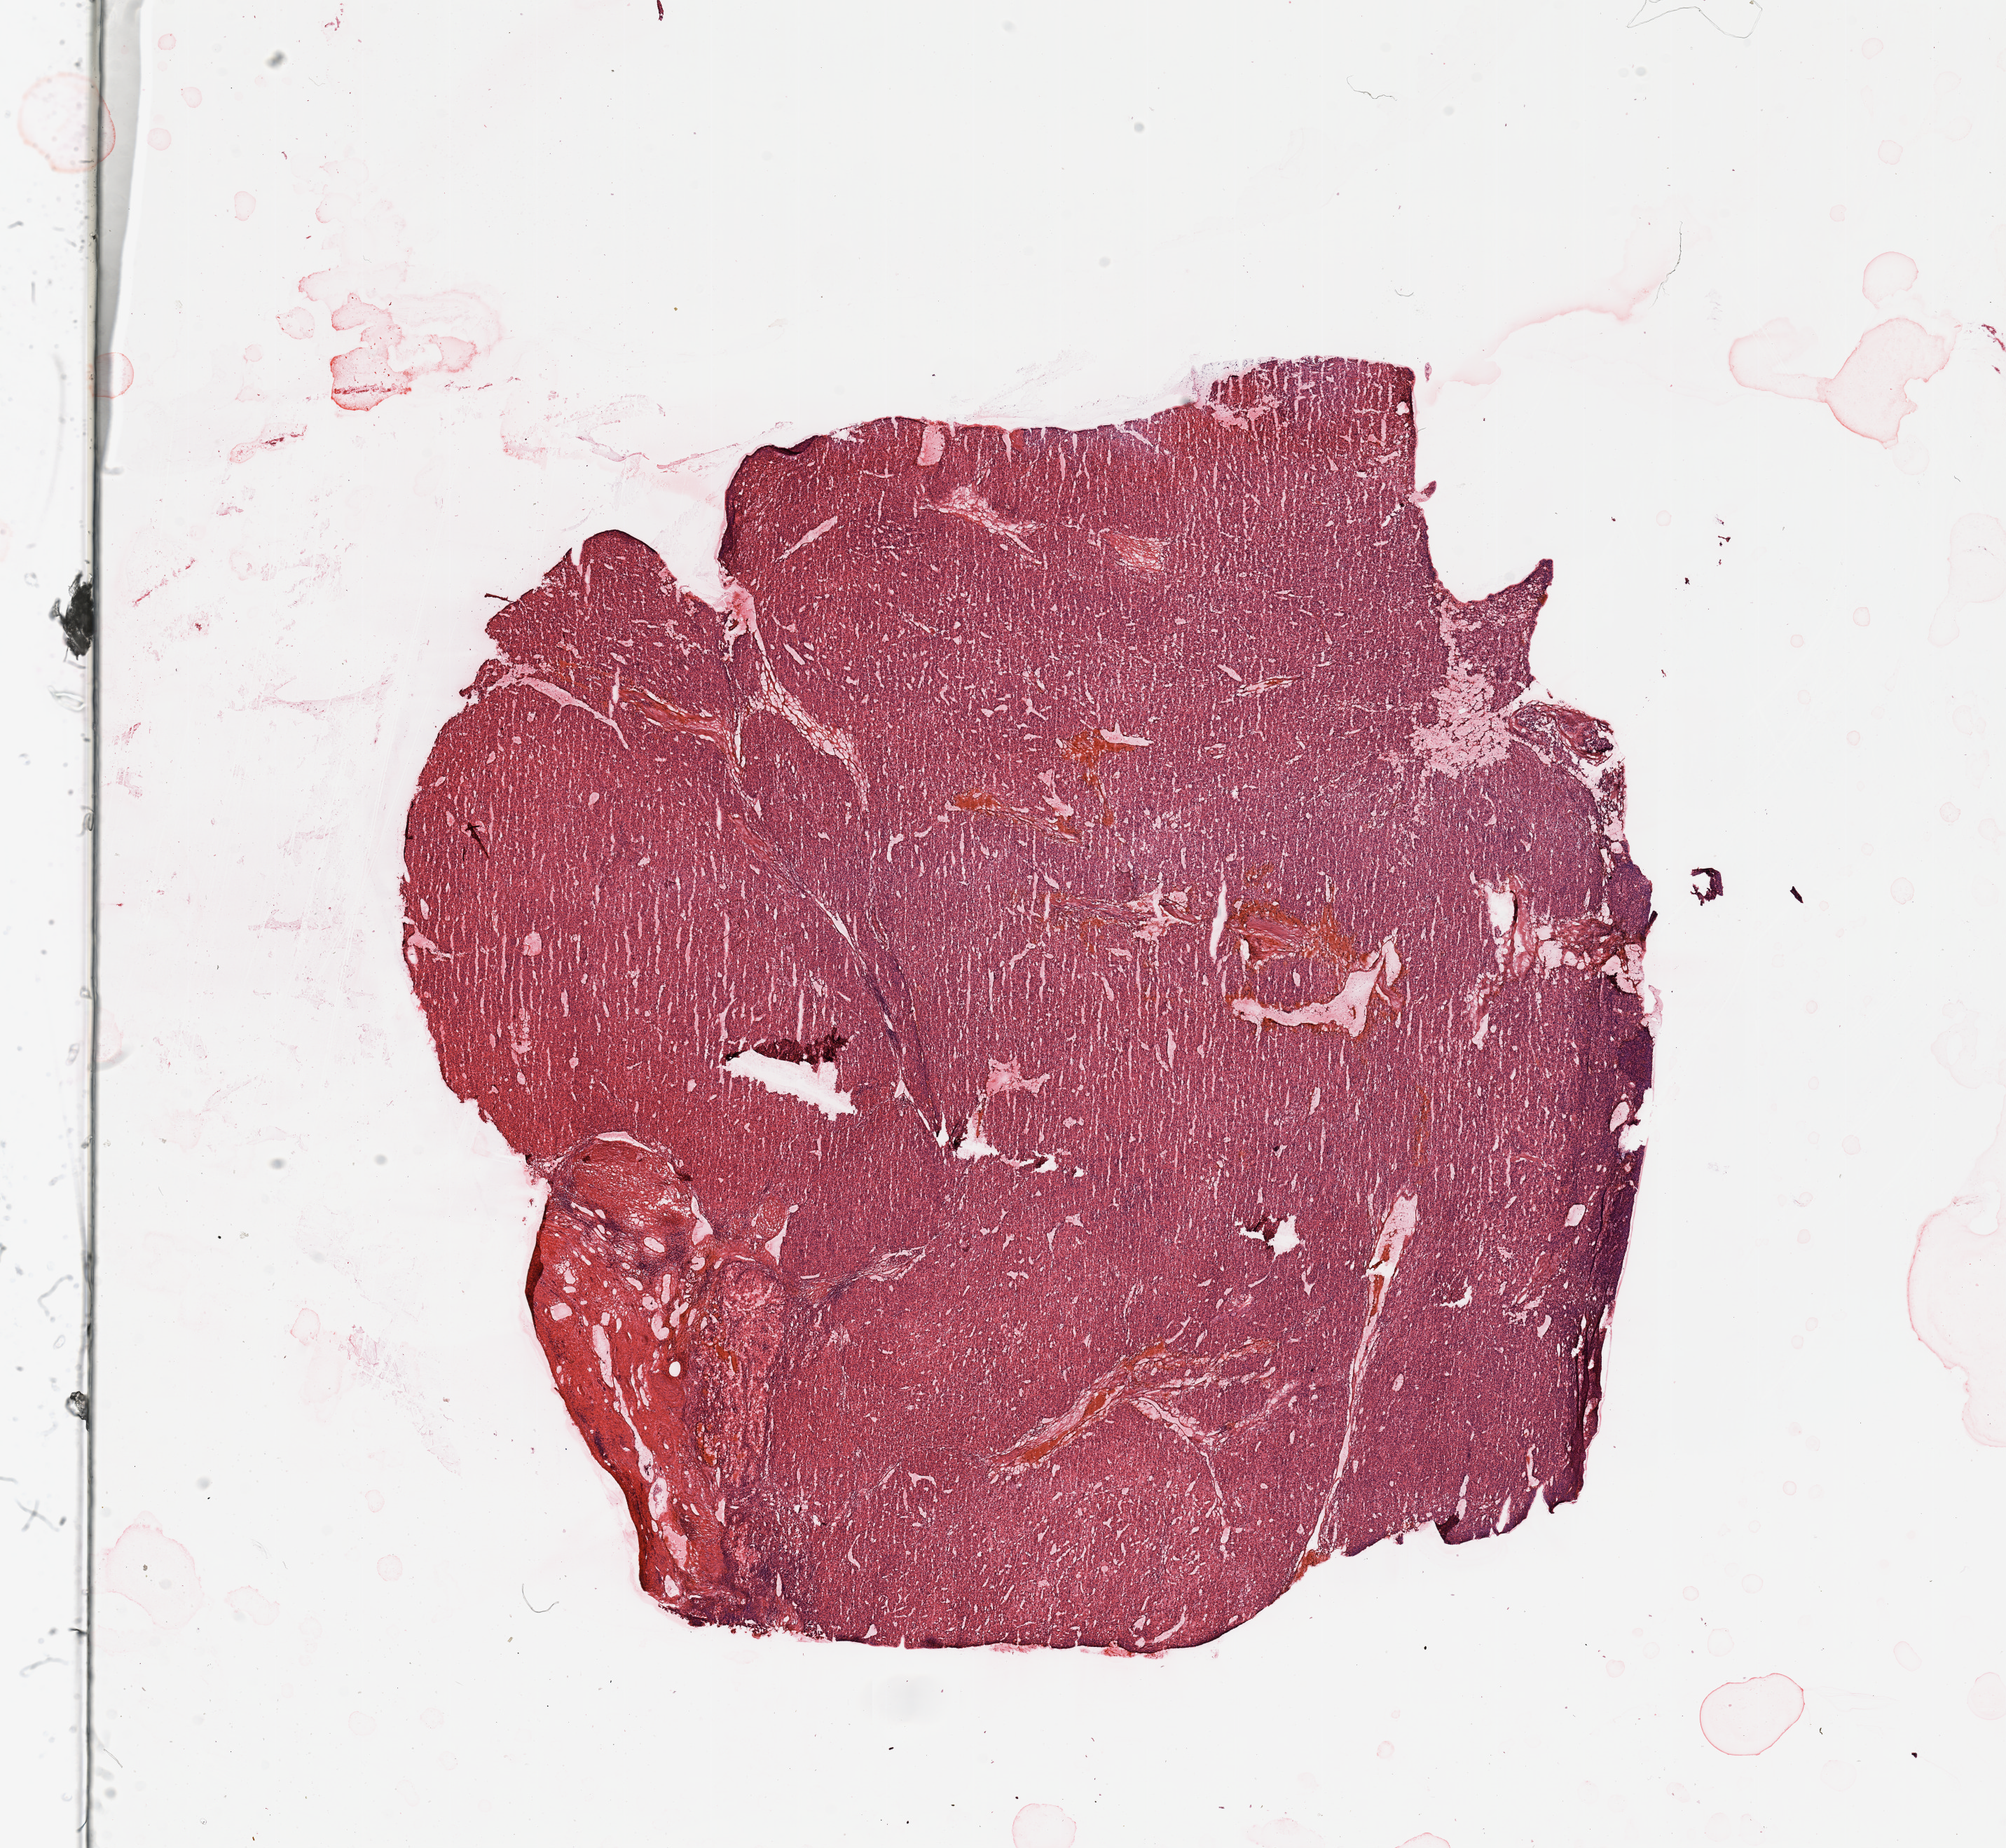
Whole-slide histology image, H&E — shown as a low-resolution overview of the whole scanned area (about 22.6 x 20.9 mm, slide scanned at 20x); tumour tissue sample, sampled site: kidney. Patient: male, age 62 years. Histologic grade: G3 (poorly differentiated). Slide review estimates, as recorded: tumour nuclei 95%, necrosis 5%.
AJCC pathologic stage: III. Diagnosis: Renal cell carcinoma, NOS.